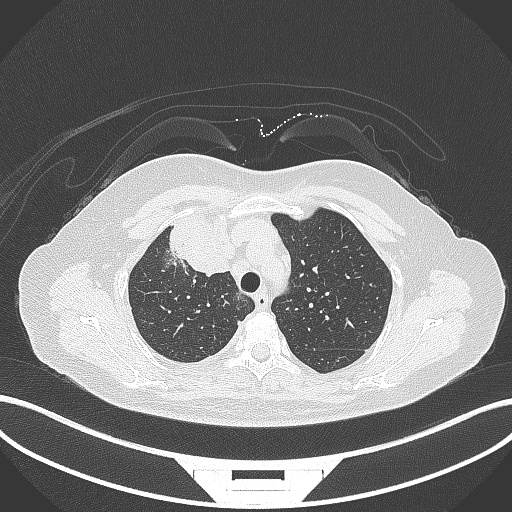
Chest CT, one axial slice. Reconstruction kernel B70f. 120 kVp. Lung window (W 1500 / L -600 HU). 512 × 512 image matrix. Patient: female, 52 years. From the clinical record (not read from this slice): clinical TNM (as recorded): T3 N1 M1.
Outlined on this slice (bounding box drawn by a radiologist):
- lung tumour (recorded histology: adenocarcinoma): bounding box (x1, y1, x2, y2) in pixels: (158, 212, 233, 282)